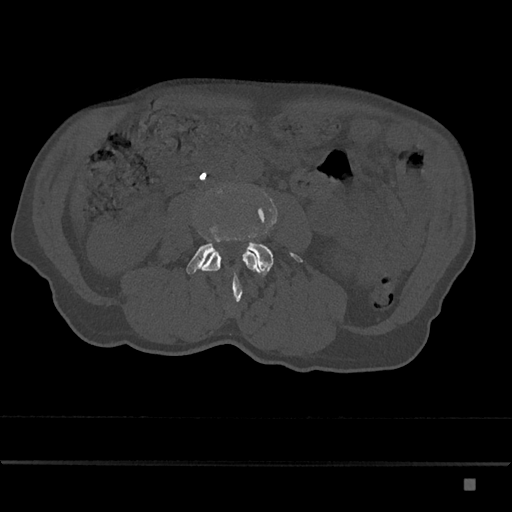
CT including the spine, one axial slice; position 371 of 797 along the scan axis; reconstruction kernel Br40s/3; bone window (W 1800 / L 400 HU); 0.5 mm slice thickness; 512 × 512 image matrix, field of view 390 × 390 mm. Patient: male, 72 years. Case-level facts recorded for this patient, not image findings: primary cancer: prostate.
Structures marked on this image (semi-automatic segmentation, software-assisted and operator-edited):
- L3 vertebra: bounding box <202,186,260,303> (left, top, right, bottom; pixels)
- L4 vertebra: <186,194,303,276>